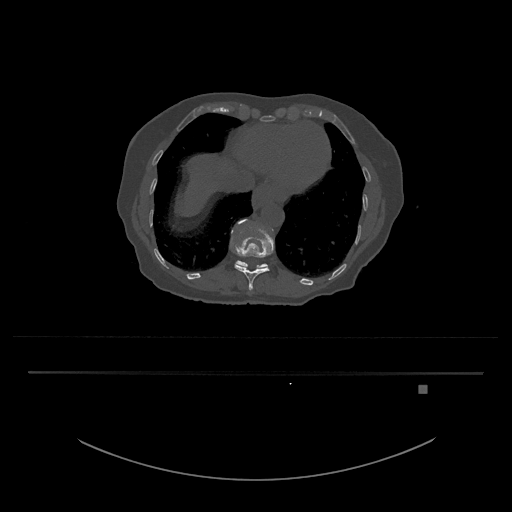
CT including the spine, one axial slice; position 650 of 797 along the scan axis; reconstruction kernel Br40s/3; bone window (W 1800 / L 400 HU); 0.5 mm slice thickness; 512 × 512 image matrix, field of view 500 × 500 mm. Patient: female, 57 years. Case-level facts recorded for this patient, not image findings: primary cancer: cervical.
Outlined on this slice (semi-automatically segmented with operator editing):
- T11 vertebra: bounding box (x1, y1, x2, y2) in pixels: (230, 219, 274, 291)
- T12 vertebra: (235, 260, 268, 269)